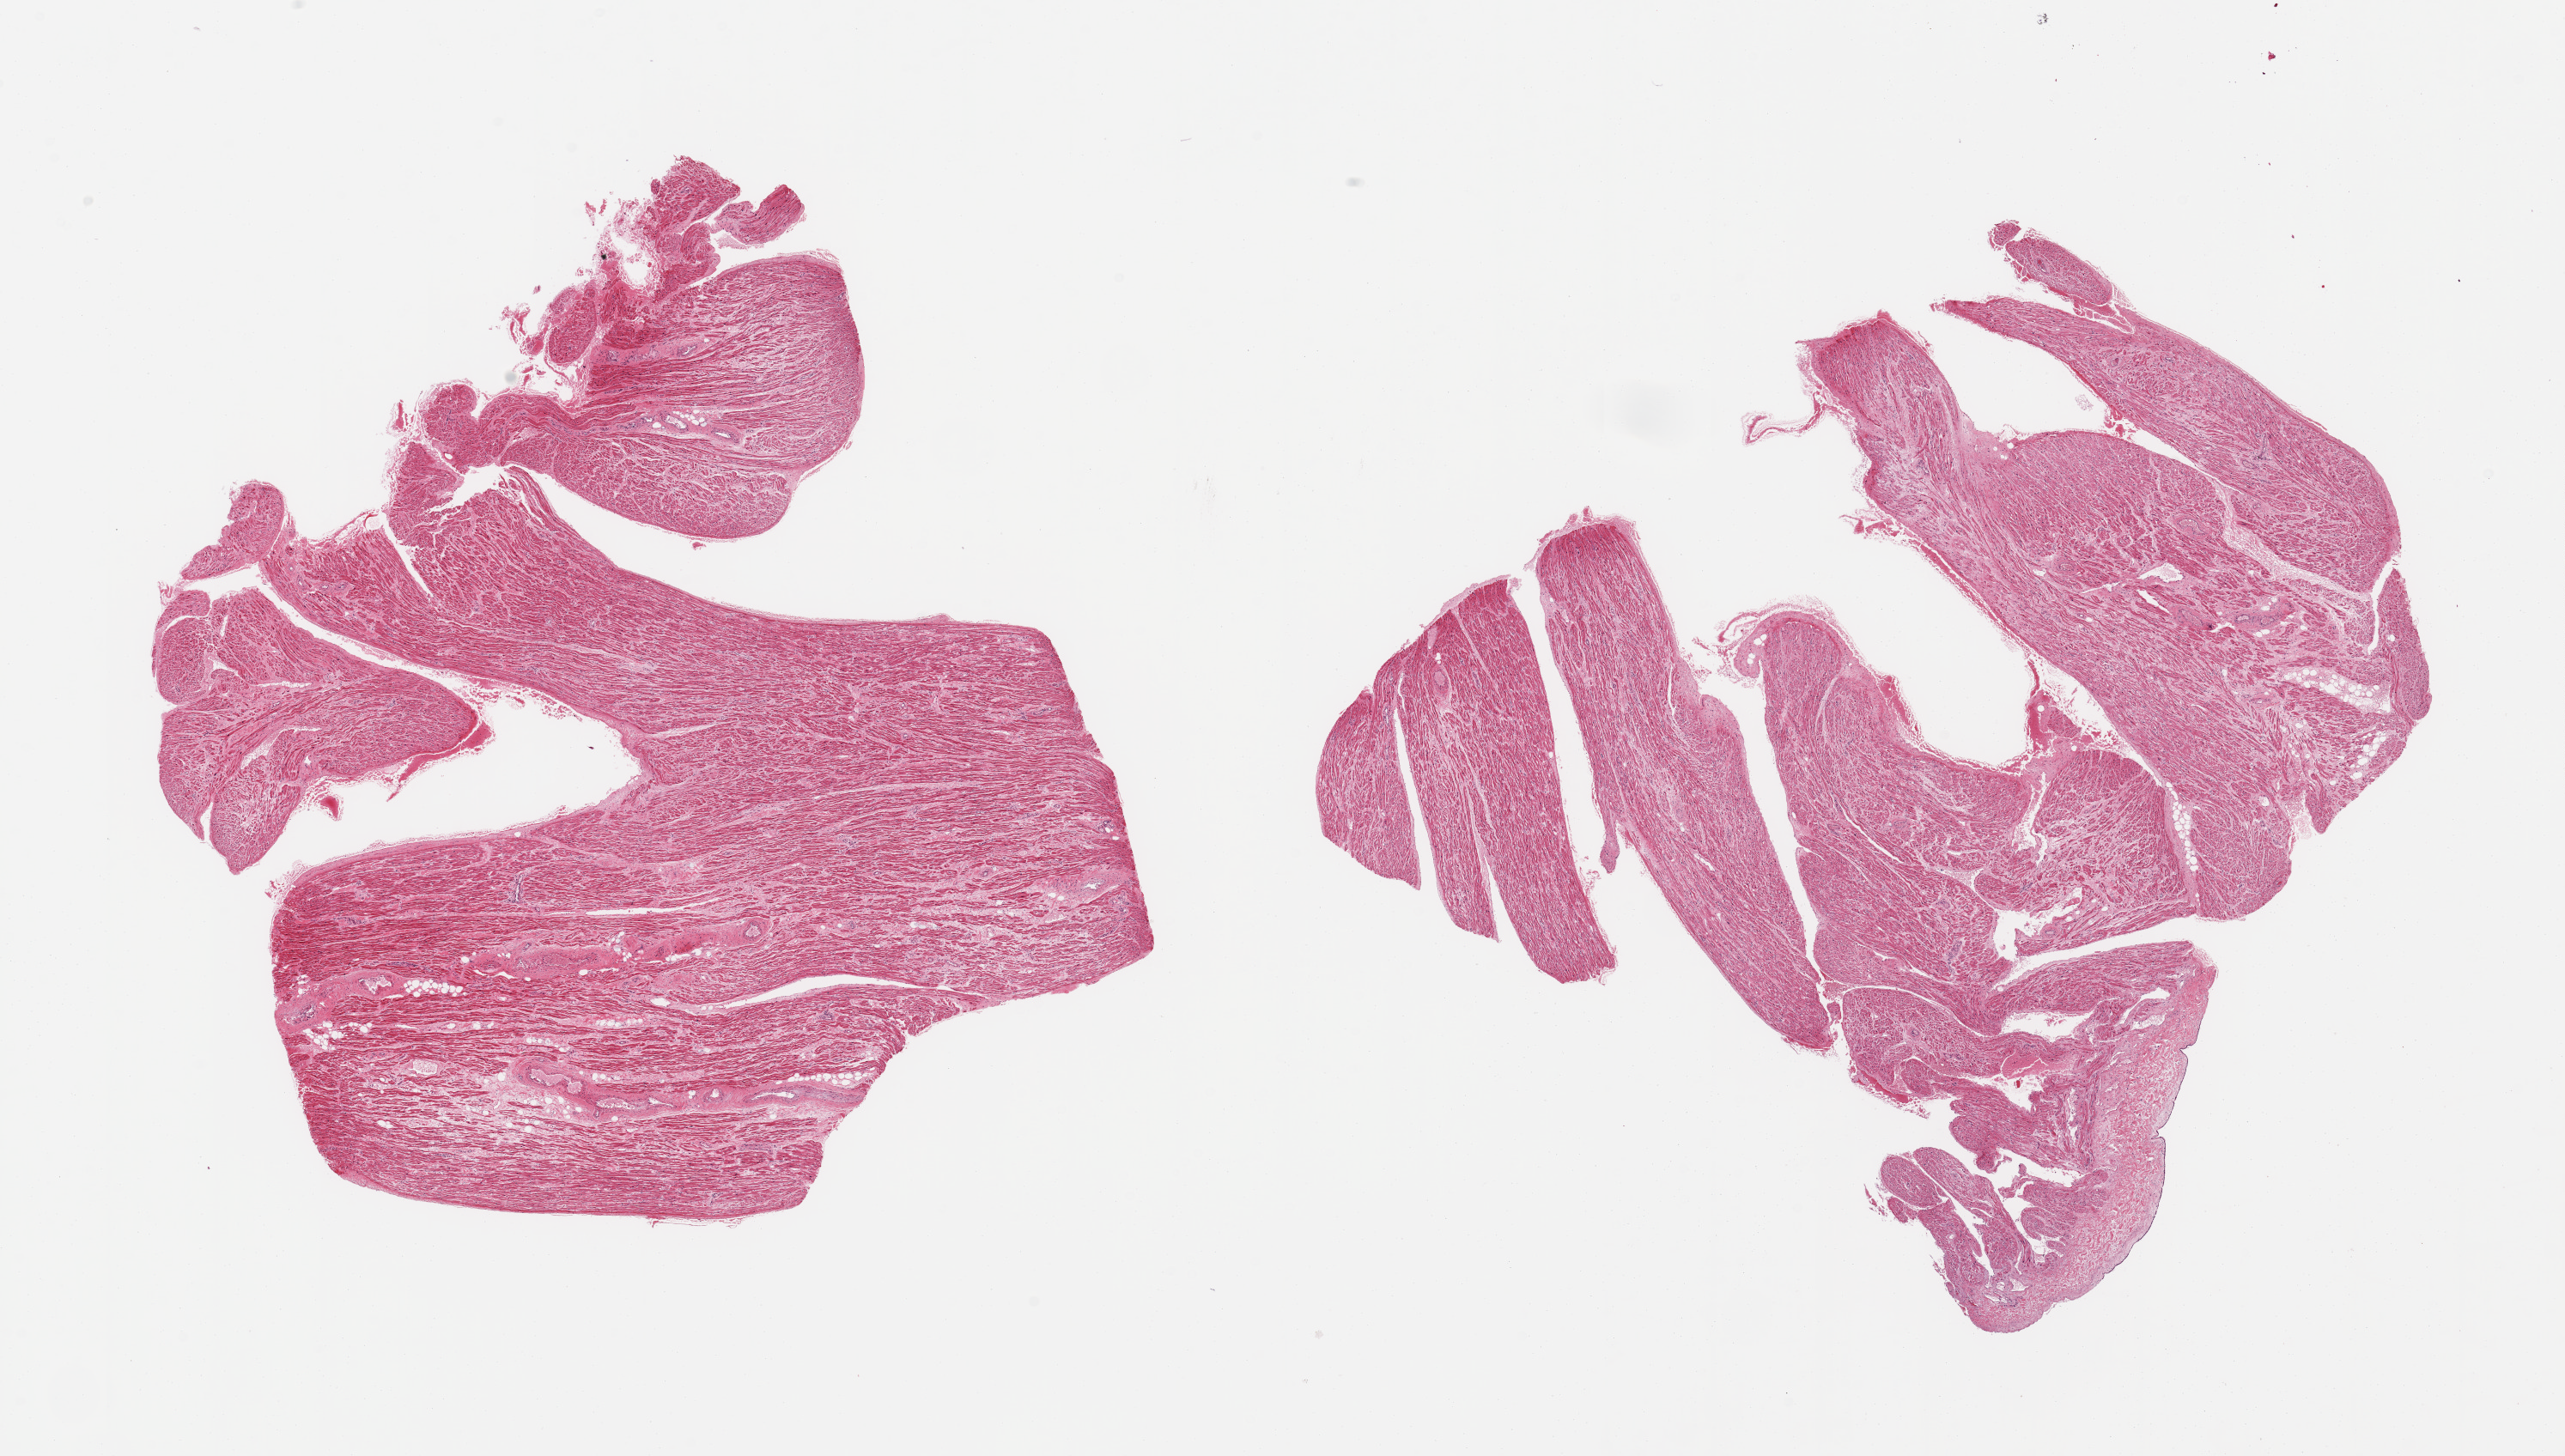
Whole-slide image, H&E stain, low-resolution overview of the scanned area, about 23.6 x 13.4 mm. PAXgene-fixed, paraffin-embedded tissue. Section of auricular appendage (target tissue). Donor tissue sample.
Reviewer comment on this tissue sample: 2 pieces; low fat & fibrous content.